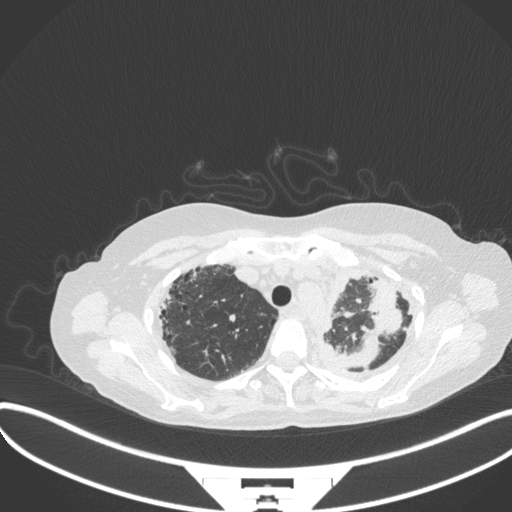
Chest CT, one axial slice. Position 276 of 373 along the scan axis. Reconstruction kernel B31f. Lung window (W 1500 / L -600 HU). 512 × 512 image matrix, field of view 400 × 400 mm. Female patient, age 56 years. From the clinical record (not read from this slice): clinical TNM (as recorded): T1 N0 M0.
Annotated regions visible in this slice (bounding box drawn by a radiologist):
- lung tumour (recorded histology: adenocarcinoma): bounding box (x1, y1, x2, y2) in pixels: (341, 277, 402, 369)